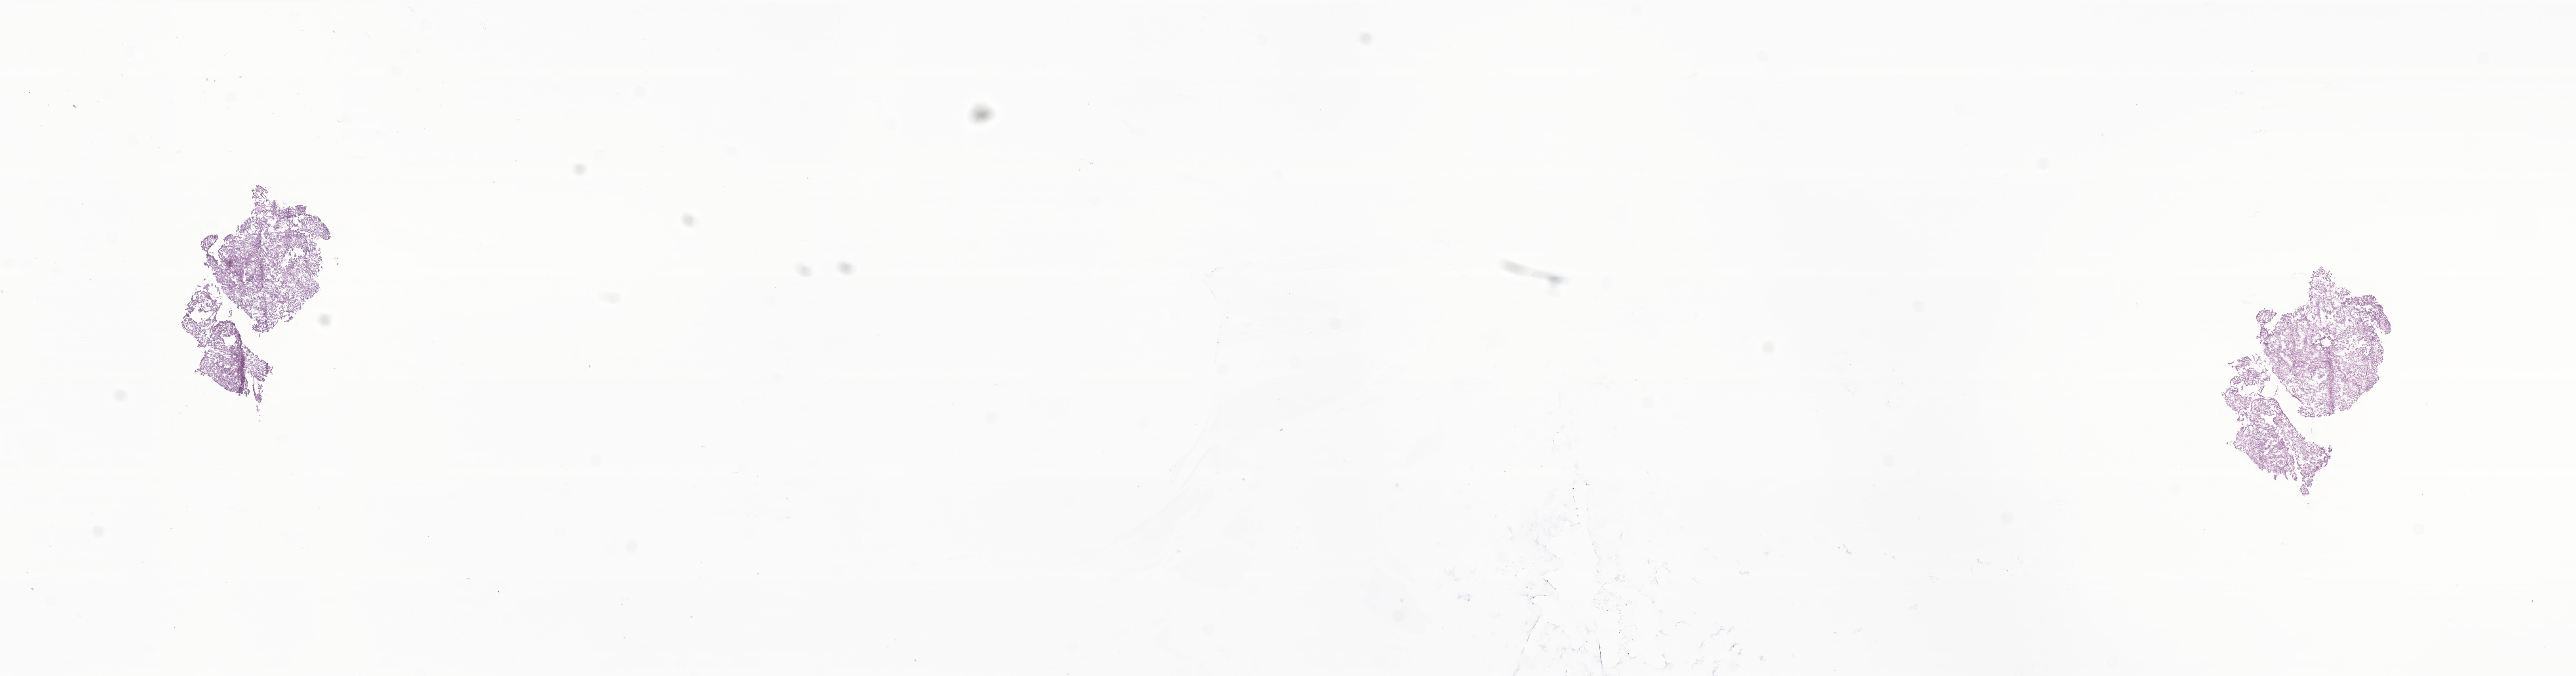
Whole-slide image, H&E stain of tumor tissue from the brain — low-resolution overview of the scanned area, about 27.4 x 7.2 mm, frozen section. Patient: female, age 55 days.
• diagnosis (ICD-O-3 morphology term): Astrocytoma, NOS